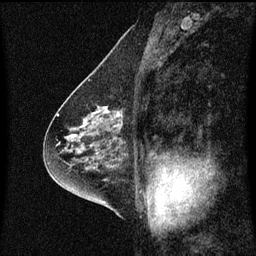
Breast MRI (dynamic contrast-enhanced), one sagittal slice. Slice 35 of 60 in the series (ordered by position). Dynamic contrast-enhanced series, image 2 of 3 at this slice position (ordered by acquisition). 1.5 T. TE 4.2 ms, TR 8.4 ms. 2 mm slice thickness. 256 × 256 image matrix, field of view 200 × 200 mm. Patient: female, 58 years.
Annotated regions visible in this slice (semi-automatic segmentation, software-assisted and operator-edited):
- analysis volume of interest (the breast-tissue region the enhancement analysis was run in; not a lesion): box from (x=86, y=106) to (x=127, y=143) px
- tumour enhancement mask (voxels above the 70 % enhancement threshold inside the analysis volume of interest): (x=91, y=106)–(x=122, y=127)